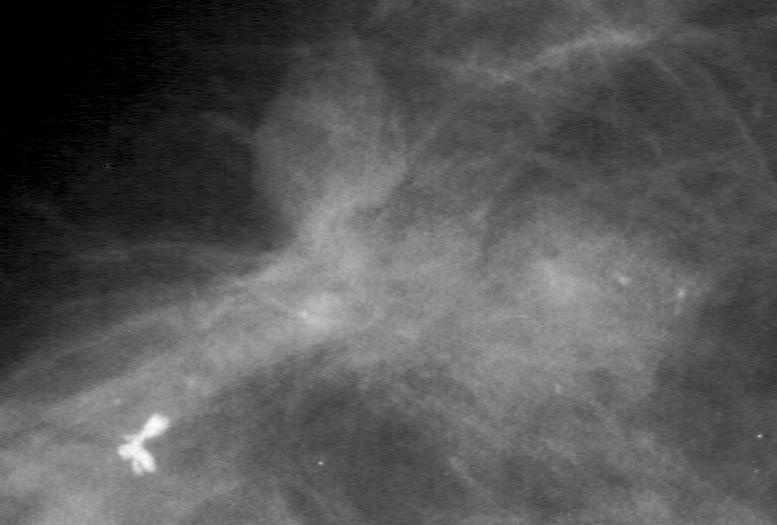
Region of interest cut from a scanned film mammogram (one marked finding); left breast; MLO view.
Marked abnormality: mass, shape irregular, margins spiculated; BI-RADS assessment category 5; subtlety rating 4 on a 1 (subtle) to 5 (obvious) scale; pathology (as recorded): malignant.